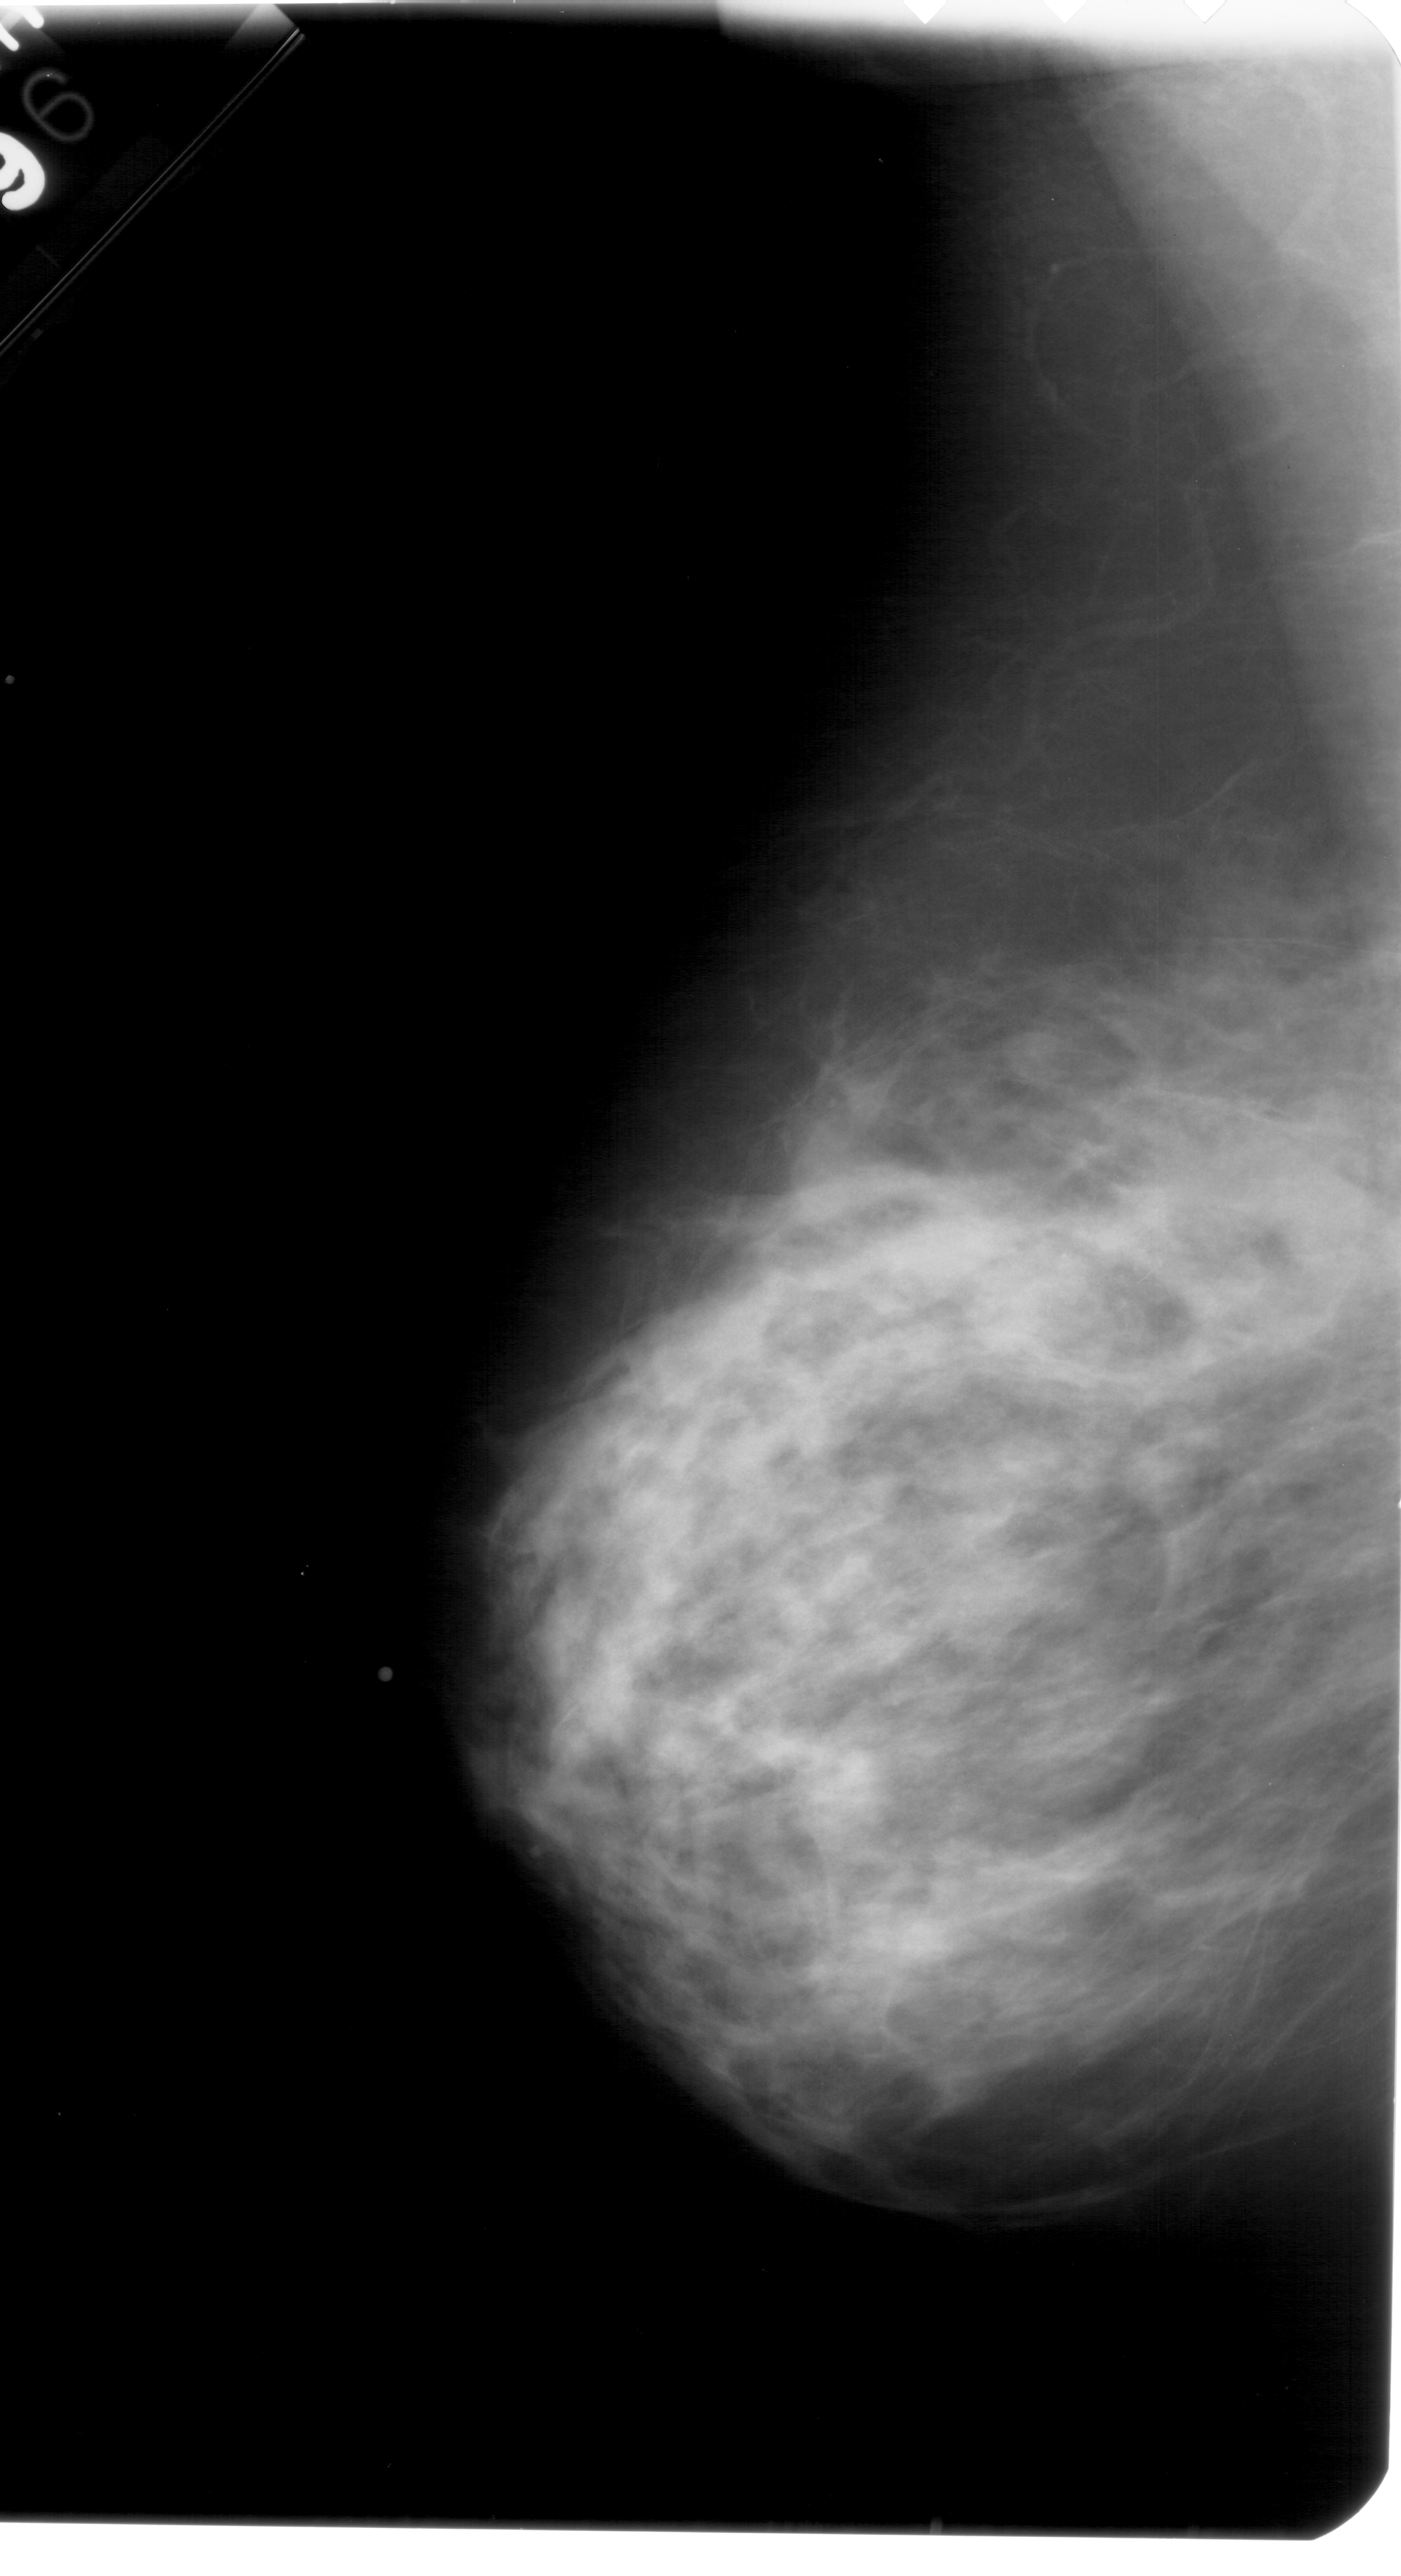
Scanned film-screen mammogram. Left breast. MLO view. Breast composition: extremely dense (BI-RADS density category 4 of 4). 1401 × 2576 image matrix.
Expert-marked regions of interest on this image (one box per marked abnormality):
- calcifications, morphology pleomorphic, distribution clustered; BI-RADS assessment category 4; subtlety rating 1 on a 1 (subtle) to 5 (obvious) scale; pathology (as recorded): malignant: bounding box (x1, y1, x2, y2) in pixels: (919, 1165, 1180, 1339)